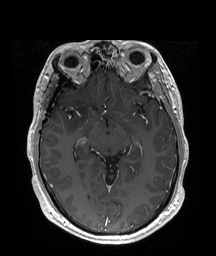
Brain MRI from a brain-tumour surgery series, one axial slice; slice 113 of 192 in the series (ordered by position); T1-weighted post-contrast; 1 mm slice thickness; 216 × 256 image matrix, field of view 219 × 260 mm. Case-level facts recorded for this patient, not image findings: histopathology: Astrocytoma; WHO grade: 2; IDH mutation: yes.
Annotated regions visible in this slice (manually delineated by an expert):
- tumour: bounding box [x1, y1, x2, y2] px = [67, 97, 92, 133]